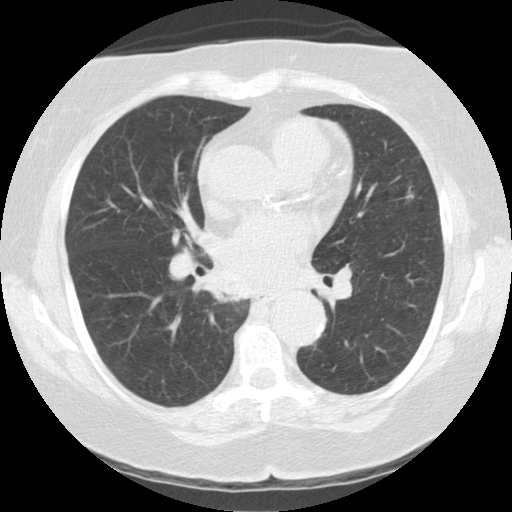
Low-dose screening chest CT, one axial slice; slice 70 of 122 in the series (ordered by position); reconstruction kernel STANDARD; lung window (W 1500 / L -600 HU); 2.5 mm slice thickness; 512 × 512 image matrix, field of view 329 × 329 mm.
Outlined on this slice (outlined manually by an expert reader):
- lesion 2 (nodule, upper lobe of left lung): bounding box (x1, y1, x2, y2) in pixels: (406, 191, 414, 199)